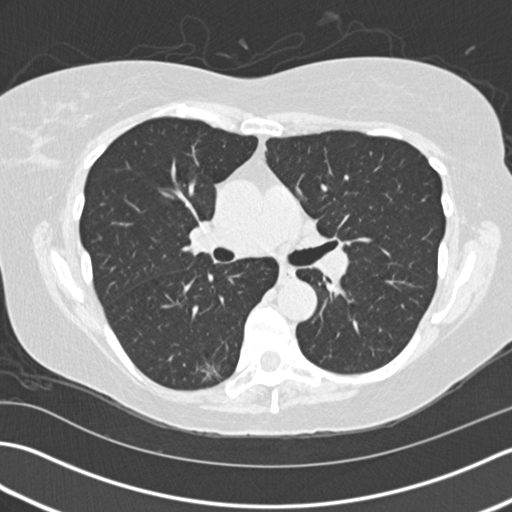
Low-dose screening chest CT, one axial slice; slice 90 of 159 in the series (ordered by position); reconstruction kernel B30f; lung window (W 1500 / L -600 HU); 2 mm slice thickness; 512 × 512 image matrix.
Annotated regions visible in this slice (outlined manually by an expert reader):
- lesion 1 (tumor, lower lobe of right lung): bounding box (x1, y1, x2, y2) in pixels: (197, 363, 220, 380)